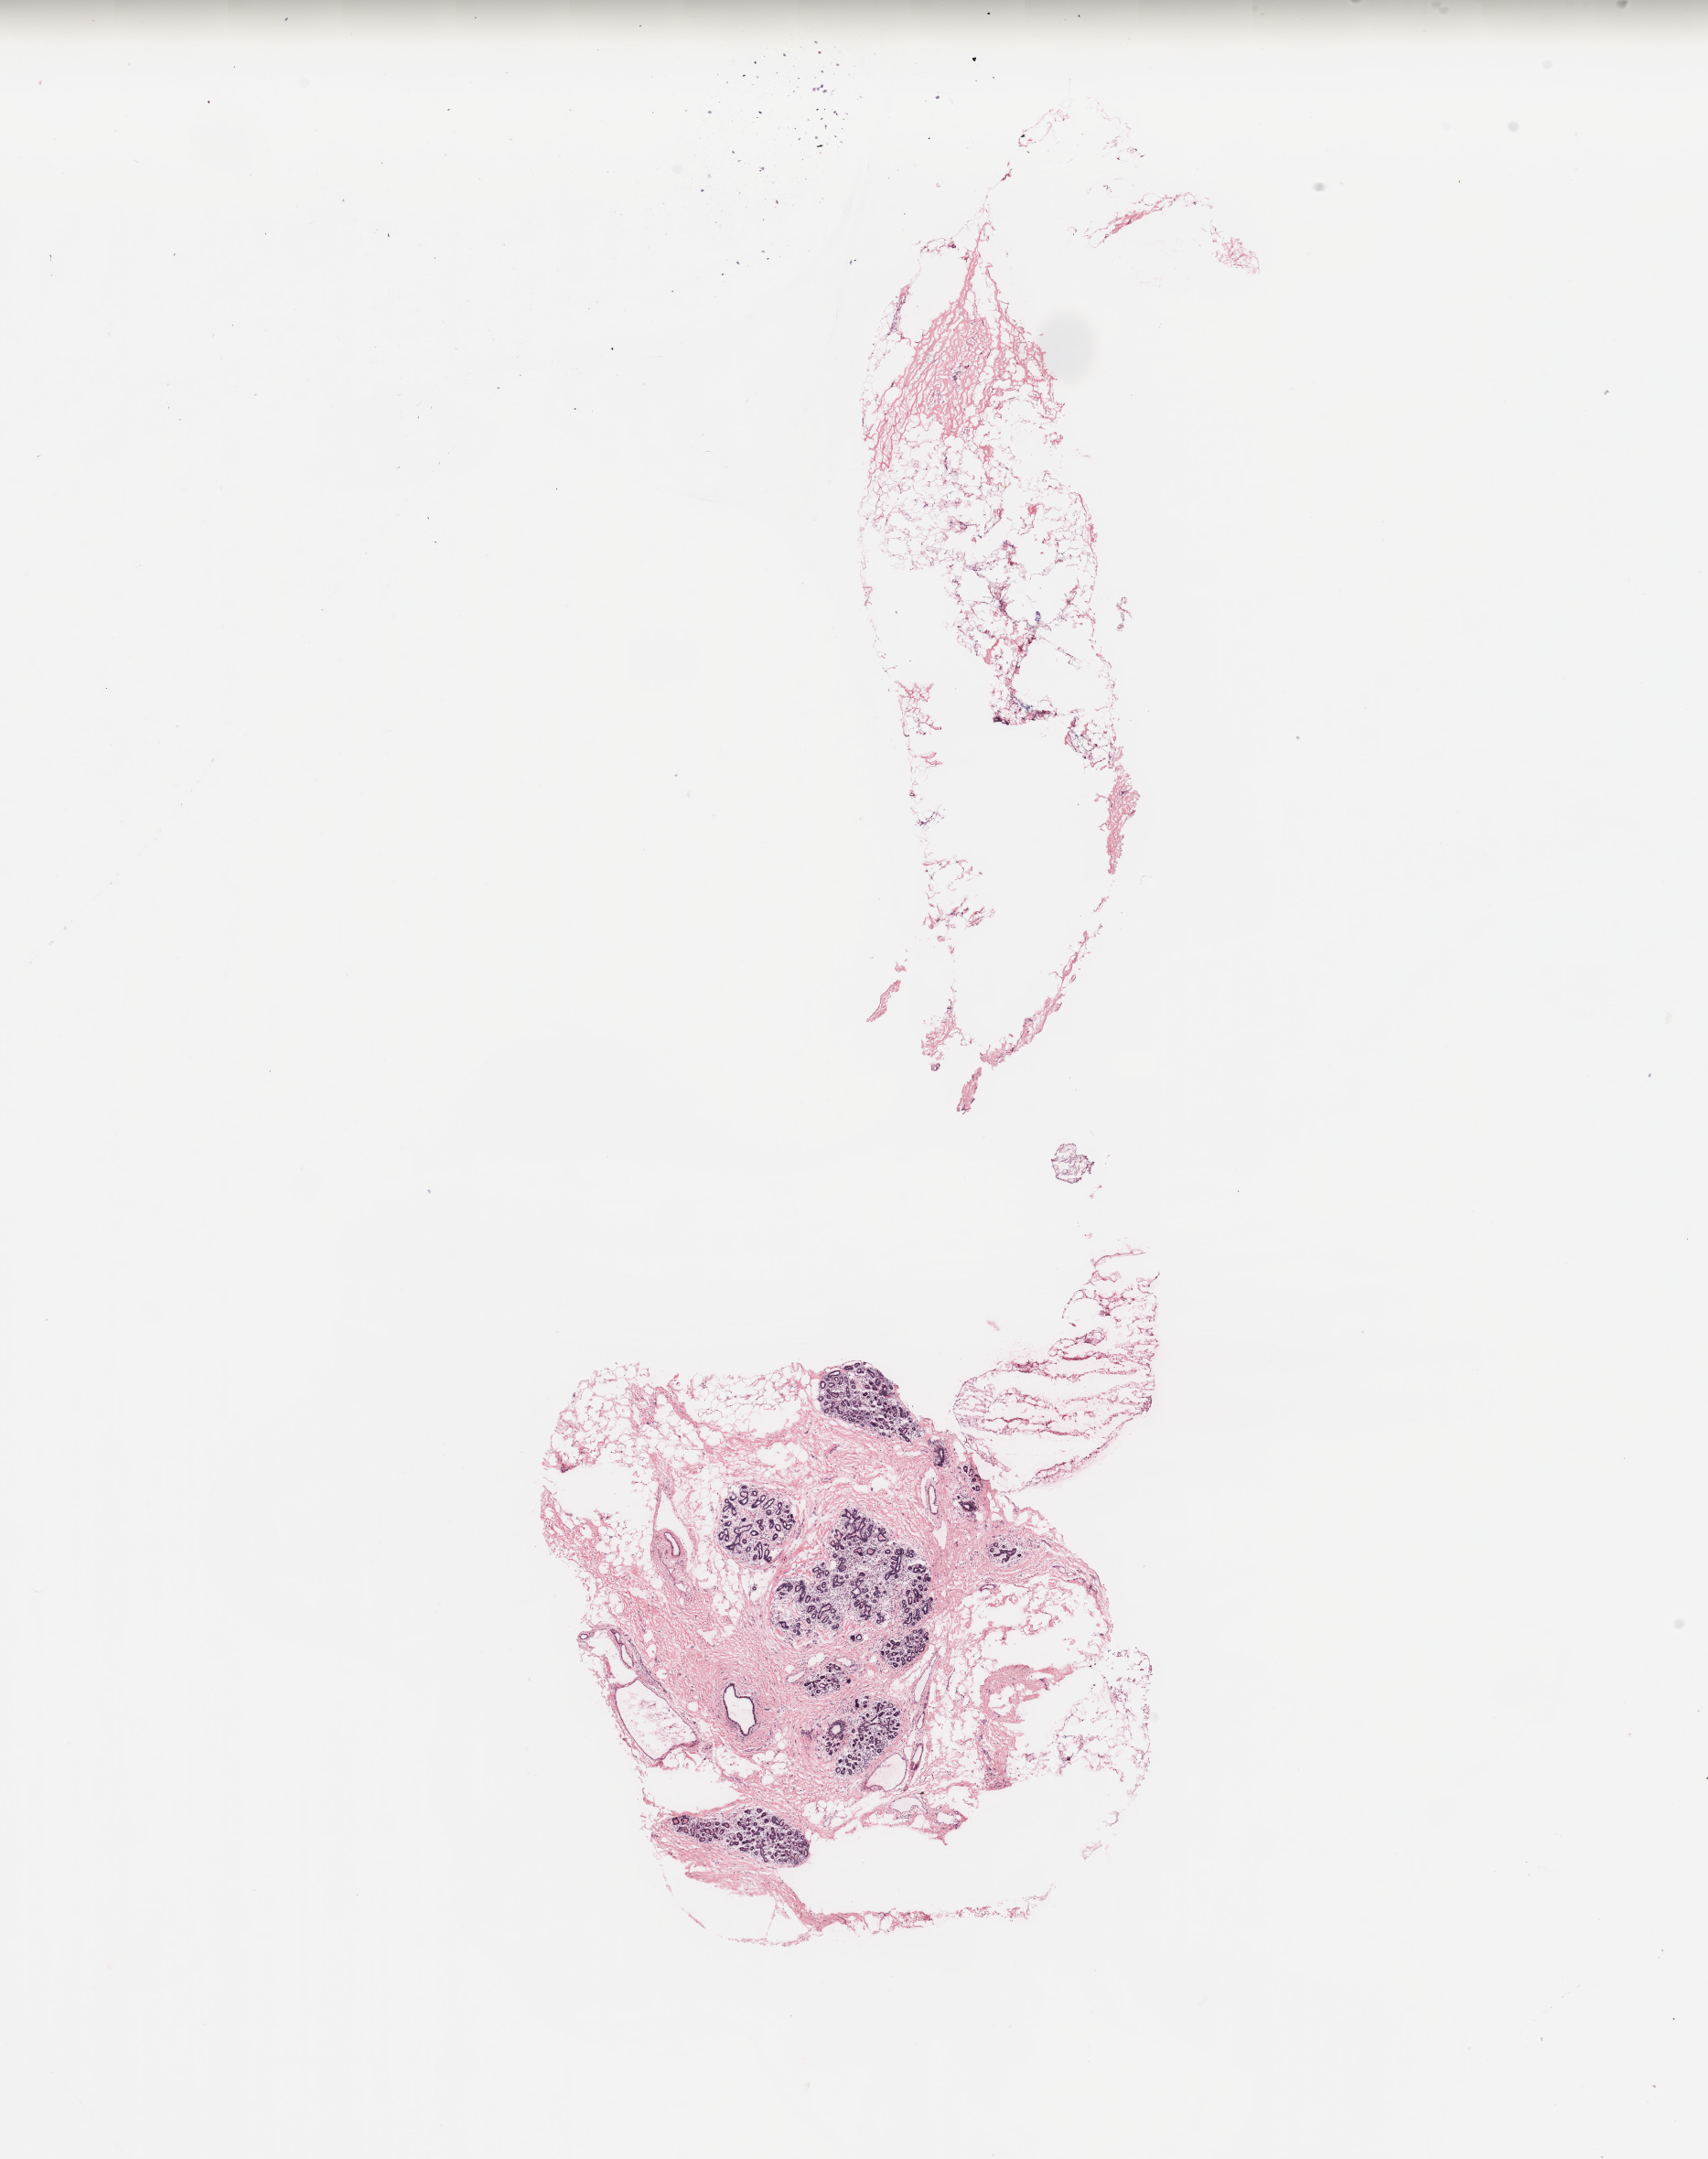
Whole-slide histology image, H&E, low-resolution overview of the scanned area, about 14.8 x 18.7 mm (slide scanned at 20x). Breast, tissue type not recorded. Patient: female, age 39 years.
Patient diagnosis: Infiltrating duct carcinoma, NOS.